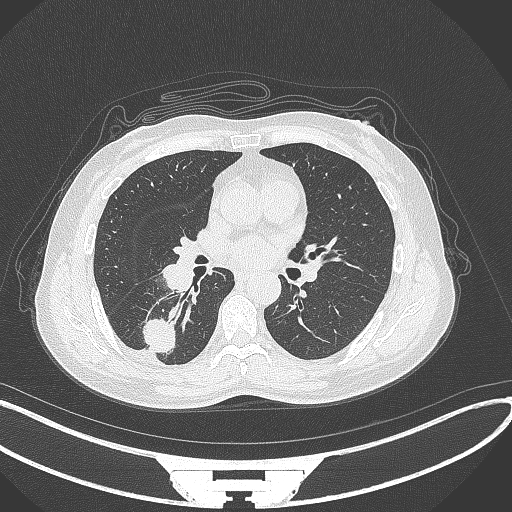
Chest CT, one axial slice; position 158 of 352 along the scan axis; reconstruction kernel B70f; 120 kVp; lung window (W 1500 / L -600 HU); 512 × 512 image matrix, field of view 400 × 400 mm. Patient: female, 55 years. From the clinical record (not read from this slice): clinical TNM (as recorded): T1c N1 M0.
Annotated regions visible in this slice (bounding box drawn by a radiologist):
- lung tumour (recorded histology: adenocarcinoma): bounding box [x1, y1, x2, y2] px = [139, 315, 179, 359]